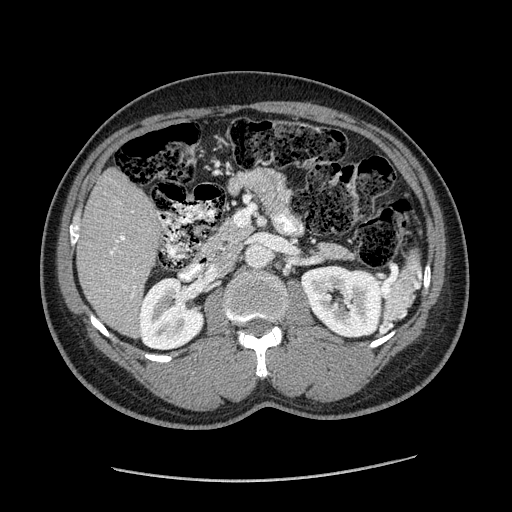
Contrast-enhanced abdominal CT (liver protocol), one axial slice. Slice 71 of 182 in the series (ordered by position). Reconstruction kernel STANDARD. 120 kVp. Soft-tissue window (W 400 / L 40 HU). 2.5 mm slice thickness. 512 × 512 image matrix, field of view 400 × 400 mm. From the clinical record (not read from this slice): diagnosis: hepatocellular carcinoma (patient treated with transarterial chemoembolisation; whether this scan precedes or follows treatment is not stated here); TNM stage (as recorded): Stage-I; Child-Pugh class: A; tumour differentiation: well differentiated; tumour nodularity: uninodular.
Structures marked on this image (semi-automatically segmented with operator editing):
- liver parenchyma outside the tumour (the mass and vessels are separate outlines, so this box may not span the whole liver): bounding box (x1, y1, x2, y2) in pixels: (76, 168, 161, 334)
- liver vessels: (110, 236, 135, 297)